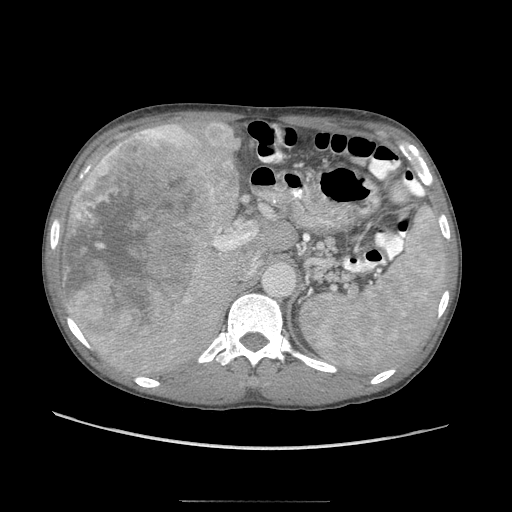
Contrast-enhanced abdominal CT (liver protocol), one axial slice; reconstruction kernel STANDARD; soft-tissue window (W 400 / L 40 HU); 512 × 512 image matrix, field of view 380 × 380 mm. From the clinical record (not read from this slice): diagnosis: hepatocellular carcinoma (patient treated with transarterial chemoembolisation; whether this scan precedes or follows treatment is not stated here); TNM stage (as recorded): Stage-IIIA; Child-Pugh class: A.
Structures marked on this image (semi-automatic segmentation, software-assisted and operator-edited):
- liver parenchyma outside the tumour (the mass and vessels are separate outlines, so this box may not span the whole liver): bounding box <56,120,266,376> (left, top, right, bottom; pixels)
- mass: <61,122,240,343>
- liver vessels: <220,251,222,253>